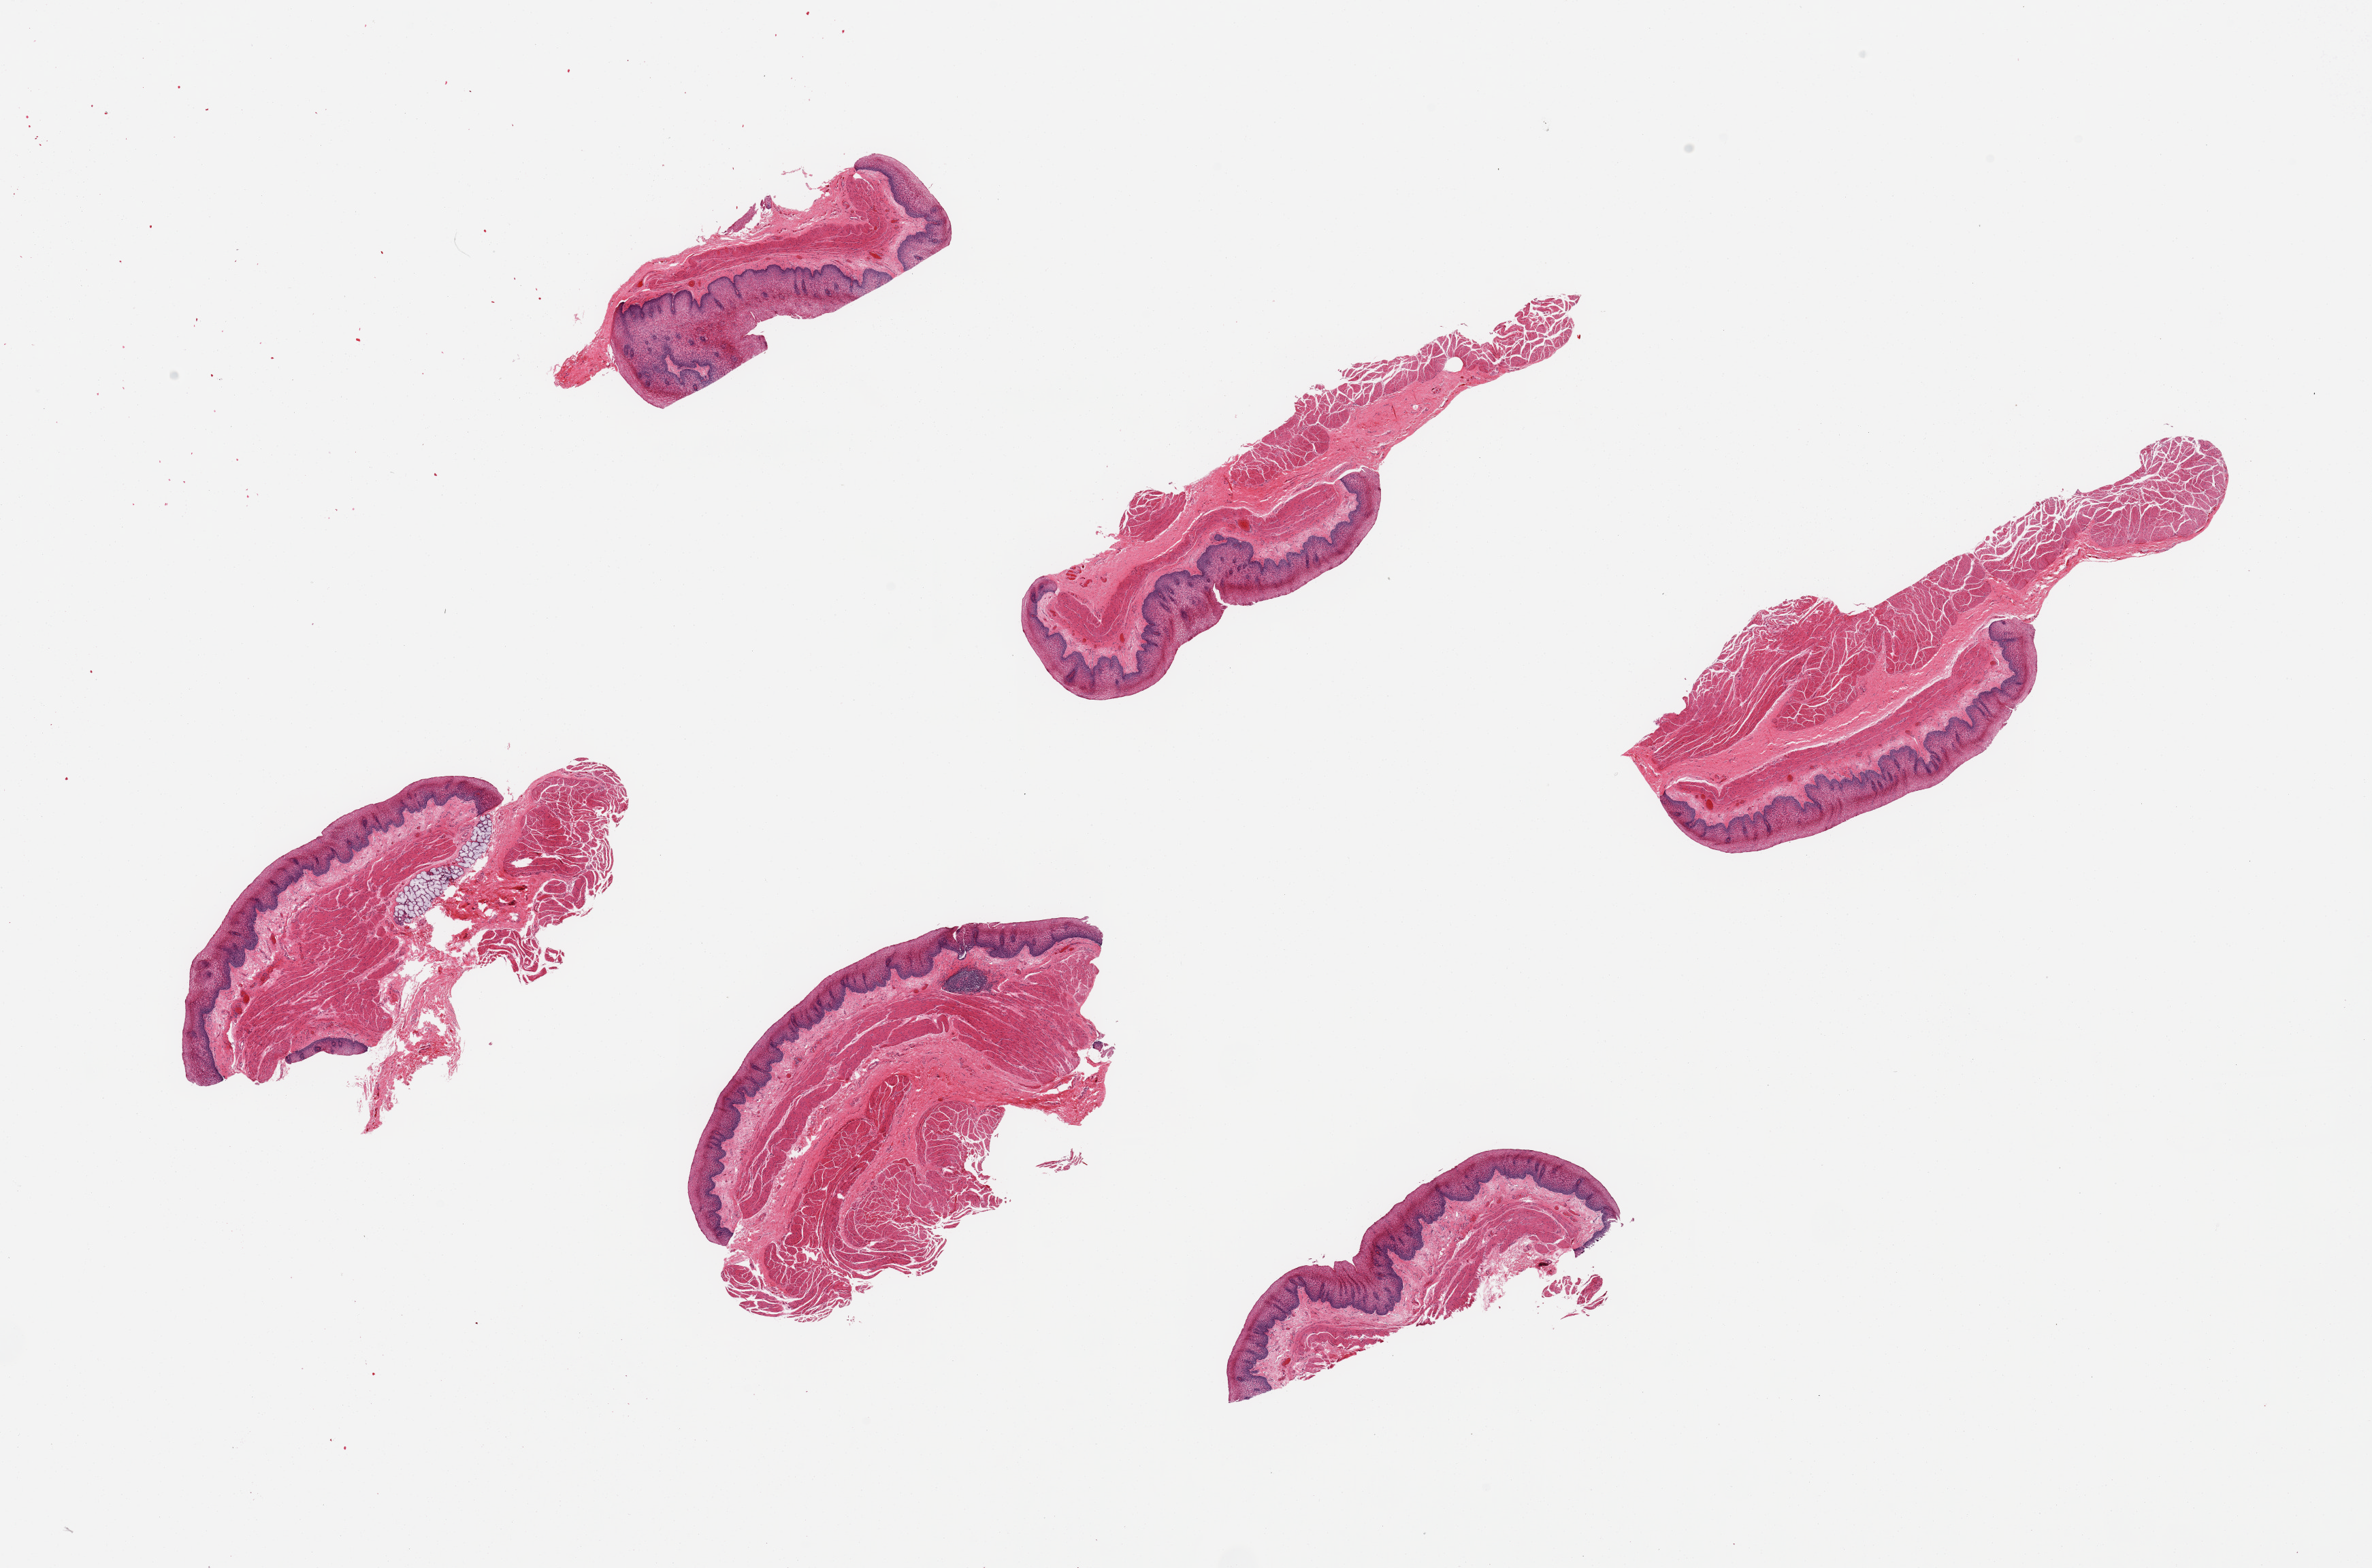
Digitized hematoxylin and eosin (H&E)-stained section — whole scanned area (about 27.6 x 18.2 mm, from a 20x scan) shown as a low-resolution overview; PAXgene-fixed paraffin-embedded (PFPE) section; sampled site (target tissue): esophageal mucous membrane; donor tissue sample. Female donor.
Pathologist's review note for this sample: 6 pieces, several pieces include muscularis propria (some marked).